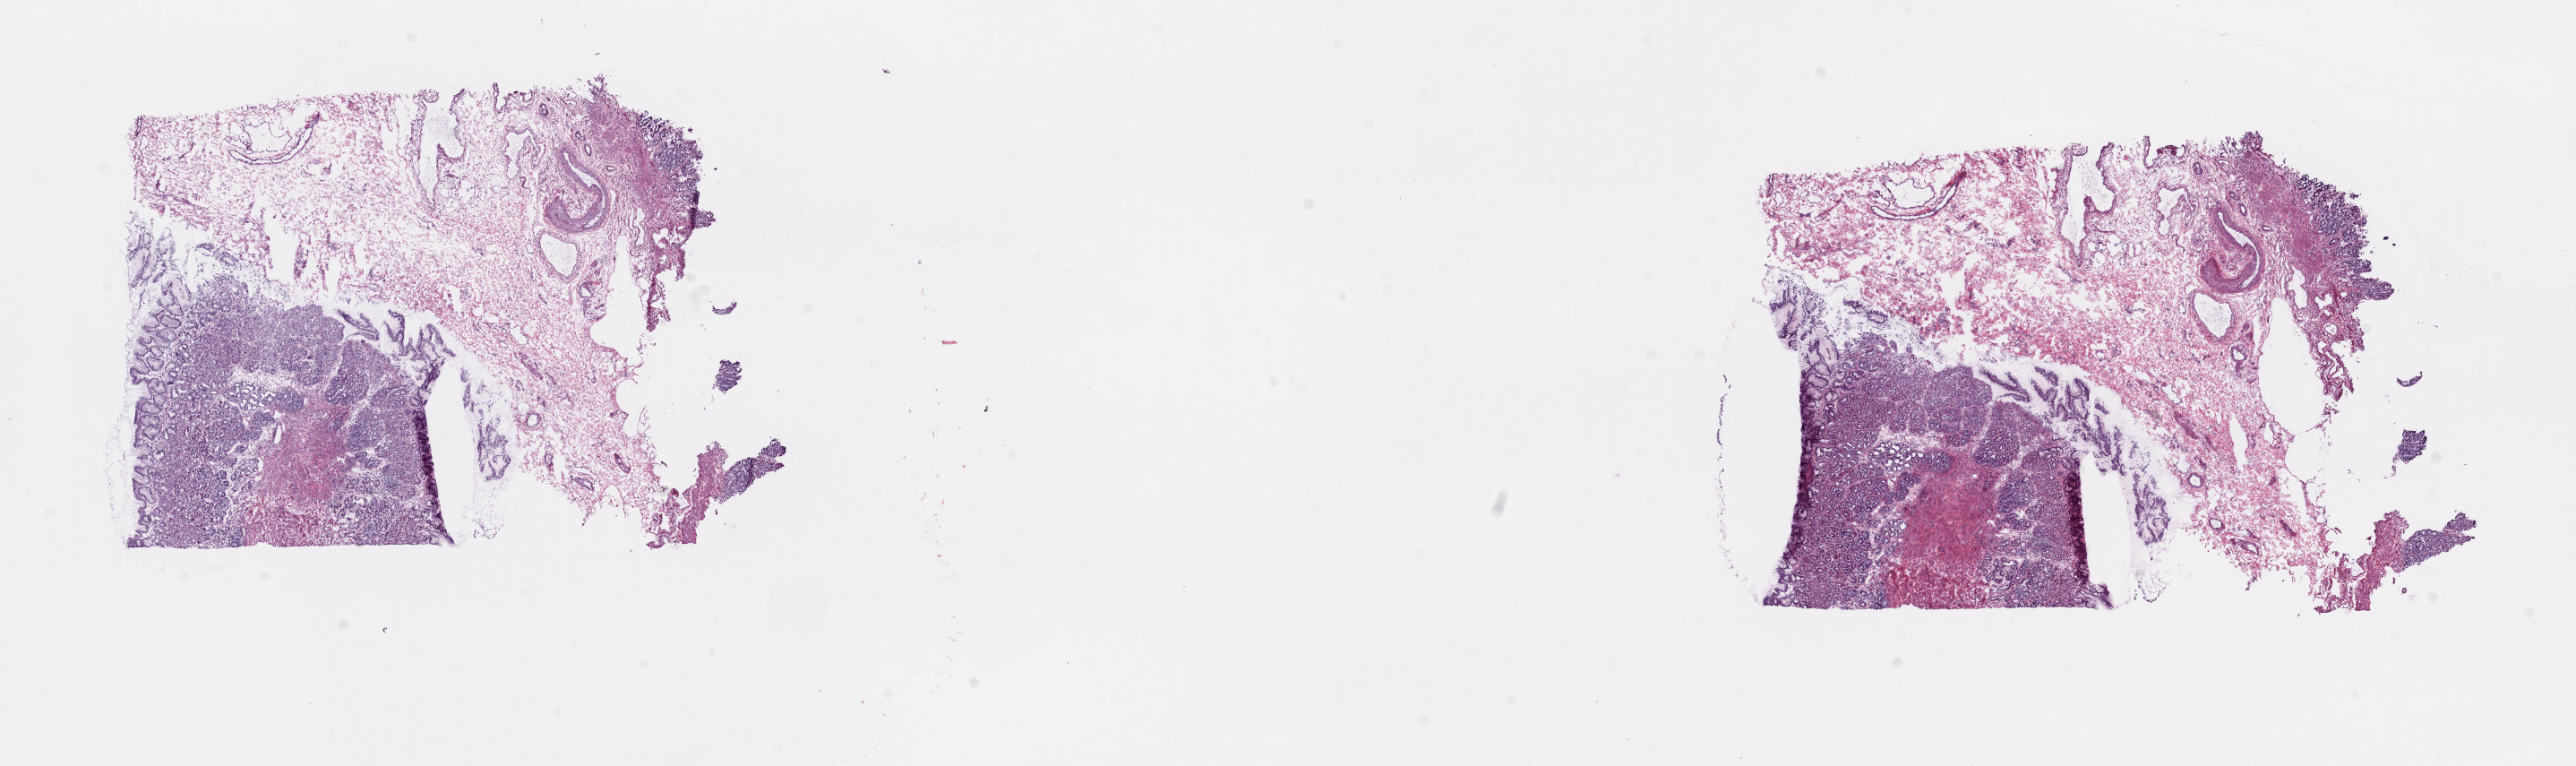
H&E-stained whole-slide image — a low-resolution overview of the entire scanned area, about 22.8 x 6.8 mm. Frozen section. Sample: solid tissue normal (non-tumour tissue), esophagus. Female patient; age at initial diagnosis 84 years. Slide review estimates, as recorded: tumour cells 0%, tumour nuclei 0%, normal cells 100%, stromal cells 0%, necrosis 0%. Inflammatory infiltration, as recorded: lymphocyte infiltration 0%, monocyte infiltration 0%, neutrophil infiltration 0%.
This section: solid tissue normal sample (biorepository sample class). Patient diagnosis: Squamous cell carcinoma, NOS (middle third of esophagus).